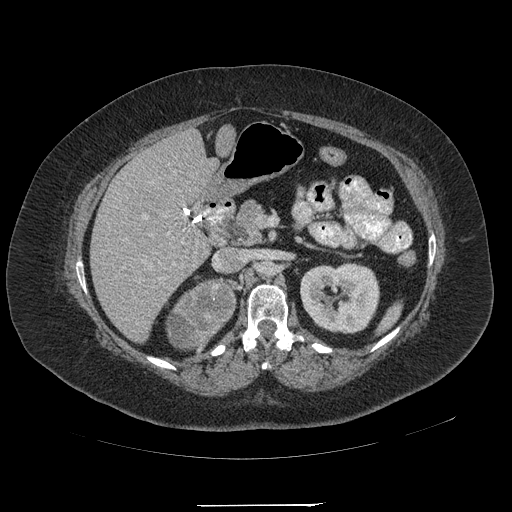
Contrast-enhanced abdominal CT, one axial slice. Position 116 of 217 along the scan axis. Intravenous contrast given. Soft-tissue window (W 400 / L 40 HU). 1.25 mm slice thickness. 512 × 512 image matrix. Female patient, age 55 years. Case-level facts recorded for this patient, not image findings: diagnosis: adrenocortical carcinoma; tumour side: right adrenal; tumour size at pathology: 11 cm; Ki-67 index: 20 %; stage (as recorded): 2.
Annotated regions visible in this slice (semi-automatically segmented with operator editing):
- mass: bounding box <168,282,234,351> (left, top, right, bottom; pixels)